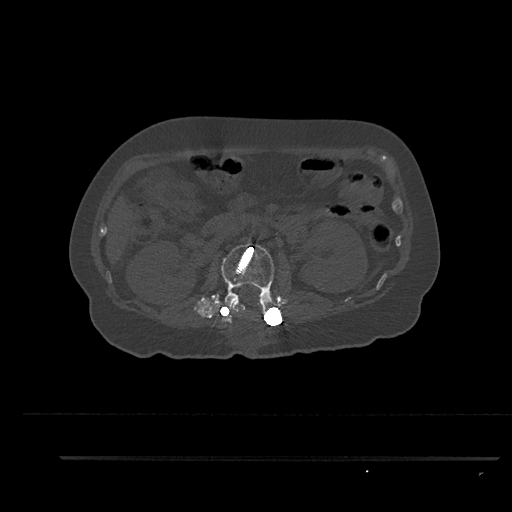
CT including the spine, one axial slice. Position 177 of 797 along the scan axis. Bone window (W 1800 / L 400 HU). 0.5 mm slice thickness. 512 × 512 image matrix, field of view 408 × 408 mm. Patient: female, 44 years. Case-level facts recorded for this patient, not image findings: primary cancer: renal; vertebrae with lytic lesions (as recorded): L1.
Structures marked on this image (semi-automatic segmentation, software-assisted and operator-edited):
- L2 vertebra: bounding box [x1, y1, x2, y2] px = [216, 242, 275, 321]